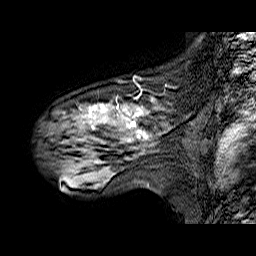
Breast MRI (dynamic contrast-enhanced), one sagittal slice; position 42 of 60 along the scan axis; dynamic contrast-enhanced series, time point 2 of 6 at this slice position (early post-contrast); 1.5 T; TE 6.3 ms, TR 32.9 ms; 4 mm slice thickness; 256 × 256 image matrix, field of view 200 × 200 mm. Female patient. Case-level facts recorded for this patient, not image findings: setting: breast cancer imaged before/during neoadjuvant chemotherapy; receptor status: HER2-positive.
Outlined on this slice (semi-automatically segmented with operator editing):
- analysis volume of interest (the breast-tissue region the enhancement analysis was run in; not a lesion): bounding box [x1, y1, x2, y2] px = [45, 86, 174, 173]
- tumour enhancement mask (voxels above the 100 % enhancement threshold inside the analysis volume of interest): [89, 104, 149, 139]